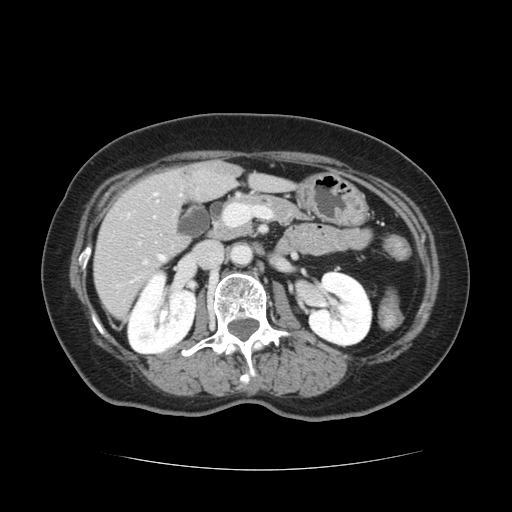
Contrast-enhanced abdominal CT, one axial slice. Slice 51 of 128 in the series (ordered by position). 120 kVp. Intravenous contrast given. Soft-tissue window (W 400 / L 40 HU). 2.5 mm slice thickness. 512 × 512 image matrix, field of view 366 × 366 mm. Female patient, age 67 years. Case-level facts recorded for this patient, not image findings: diagnosis: colorectal cancer liver metastases, imaged before liver resection.
Annotated regions visible in this slice (outlined manually by an expert reader):
- hepatic veins: bounding box <115,254,165,288> (left, top, right, bottom; pixels)
- liver: <95,162,287,317>
- planned liver remnant (the part of the liver to remain after resection): <95,174,288,317>
- portal vein (with intrahepatic branches): <112,205,242,264>